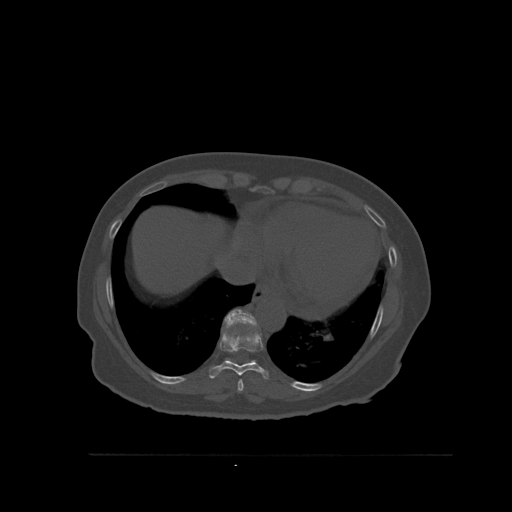
CT including the spine, one axial slice; bone window (W 1800 / L 400 HU); 1.5 mm slice thickness; 512 × 512 image matrix. Patient: female, 73 years. From the clinical record (not read from this slice): primary cancer: breast; vertebrae with lytic lesions (as recorded): L2.
Outlined on this slice (semi-automatically segmented with operator editing):
- T10 vertebra: box from (x=224, y=309) to (x=258, y=363) px
- T8 vertebra: (x=237, y=379)–(x=244, y=392)
- T9 vertebra: (x=209, y=328)–(x=269, y=380)